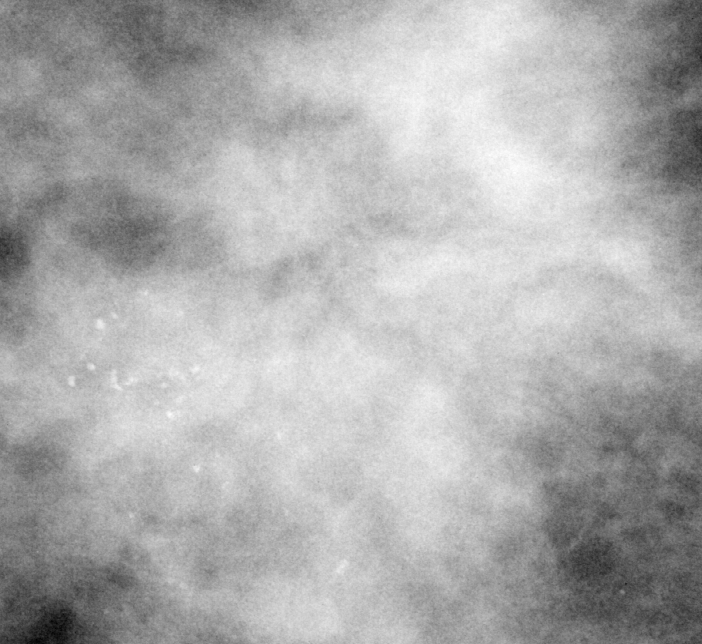
Crop from a digitized film mammogram around one marked abnormality, right breast, CC view.
- Mass, shape architectural distortion, margins ill defined; BI-RADS assessment category 4; pathology (as recorded): malignant.